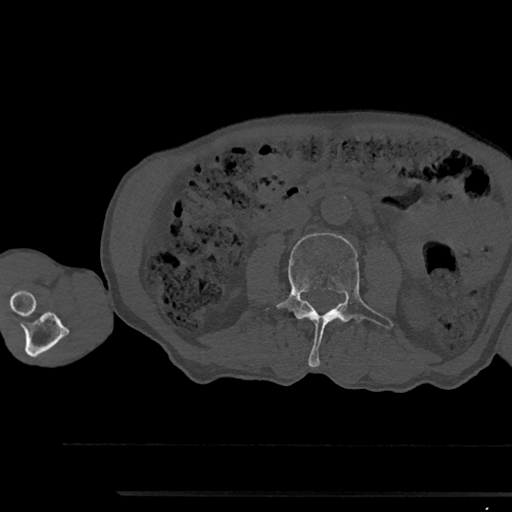
CT including the spine, one axial slice. Slice 493 of 797 in the series (ordered by position). Bone window (W 1800 / L 400 HU). 0.5 mm slice thickness. 512 × 512 image matrix. Male patient, age 79 years. From the clinical record (not read from this slice): primary cancer: prostate.
Structures marked on this image (semi-automatic segmentation, software-assisted and operator-edited):
- L3 vertebra: bounding box <277,233,393,367> (left, top, right, bottom; pixels)